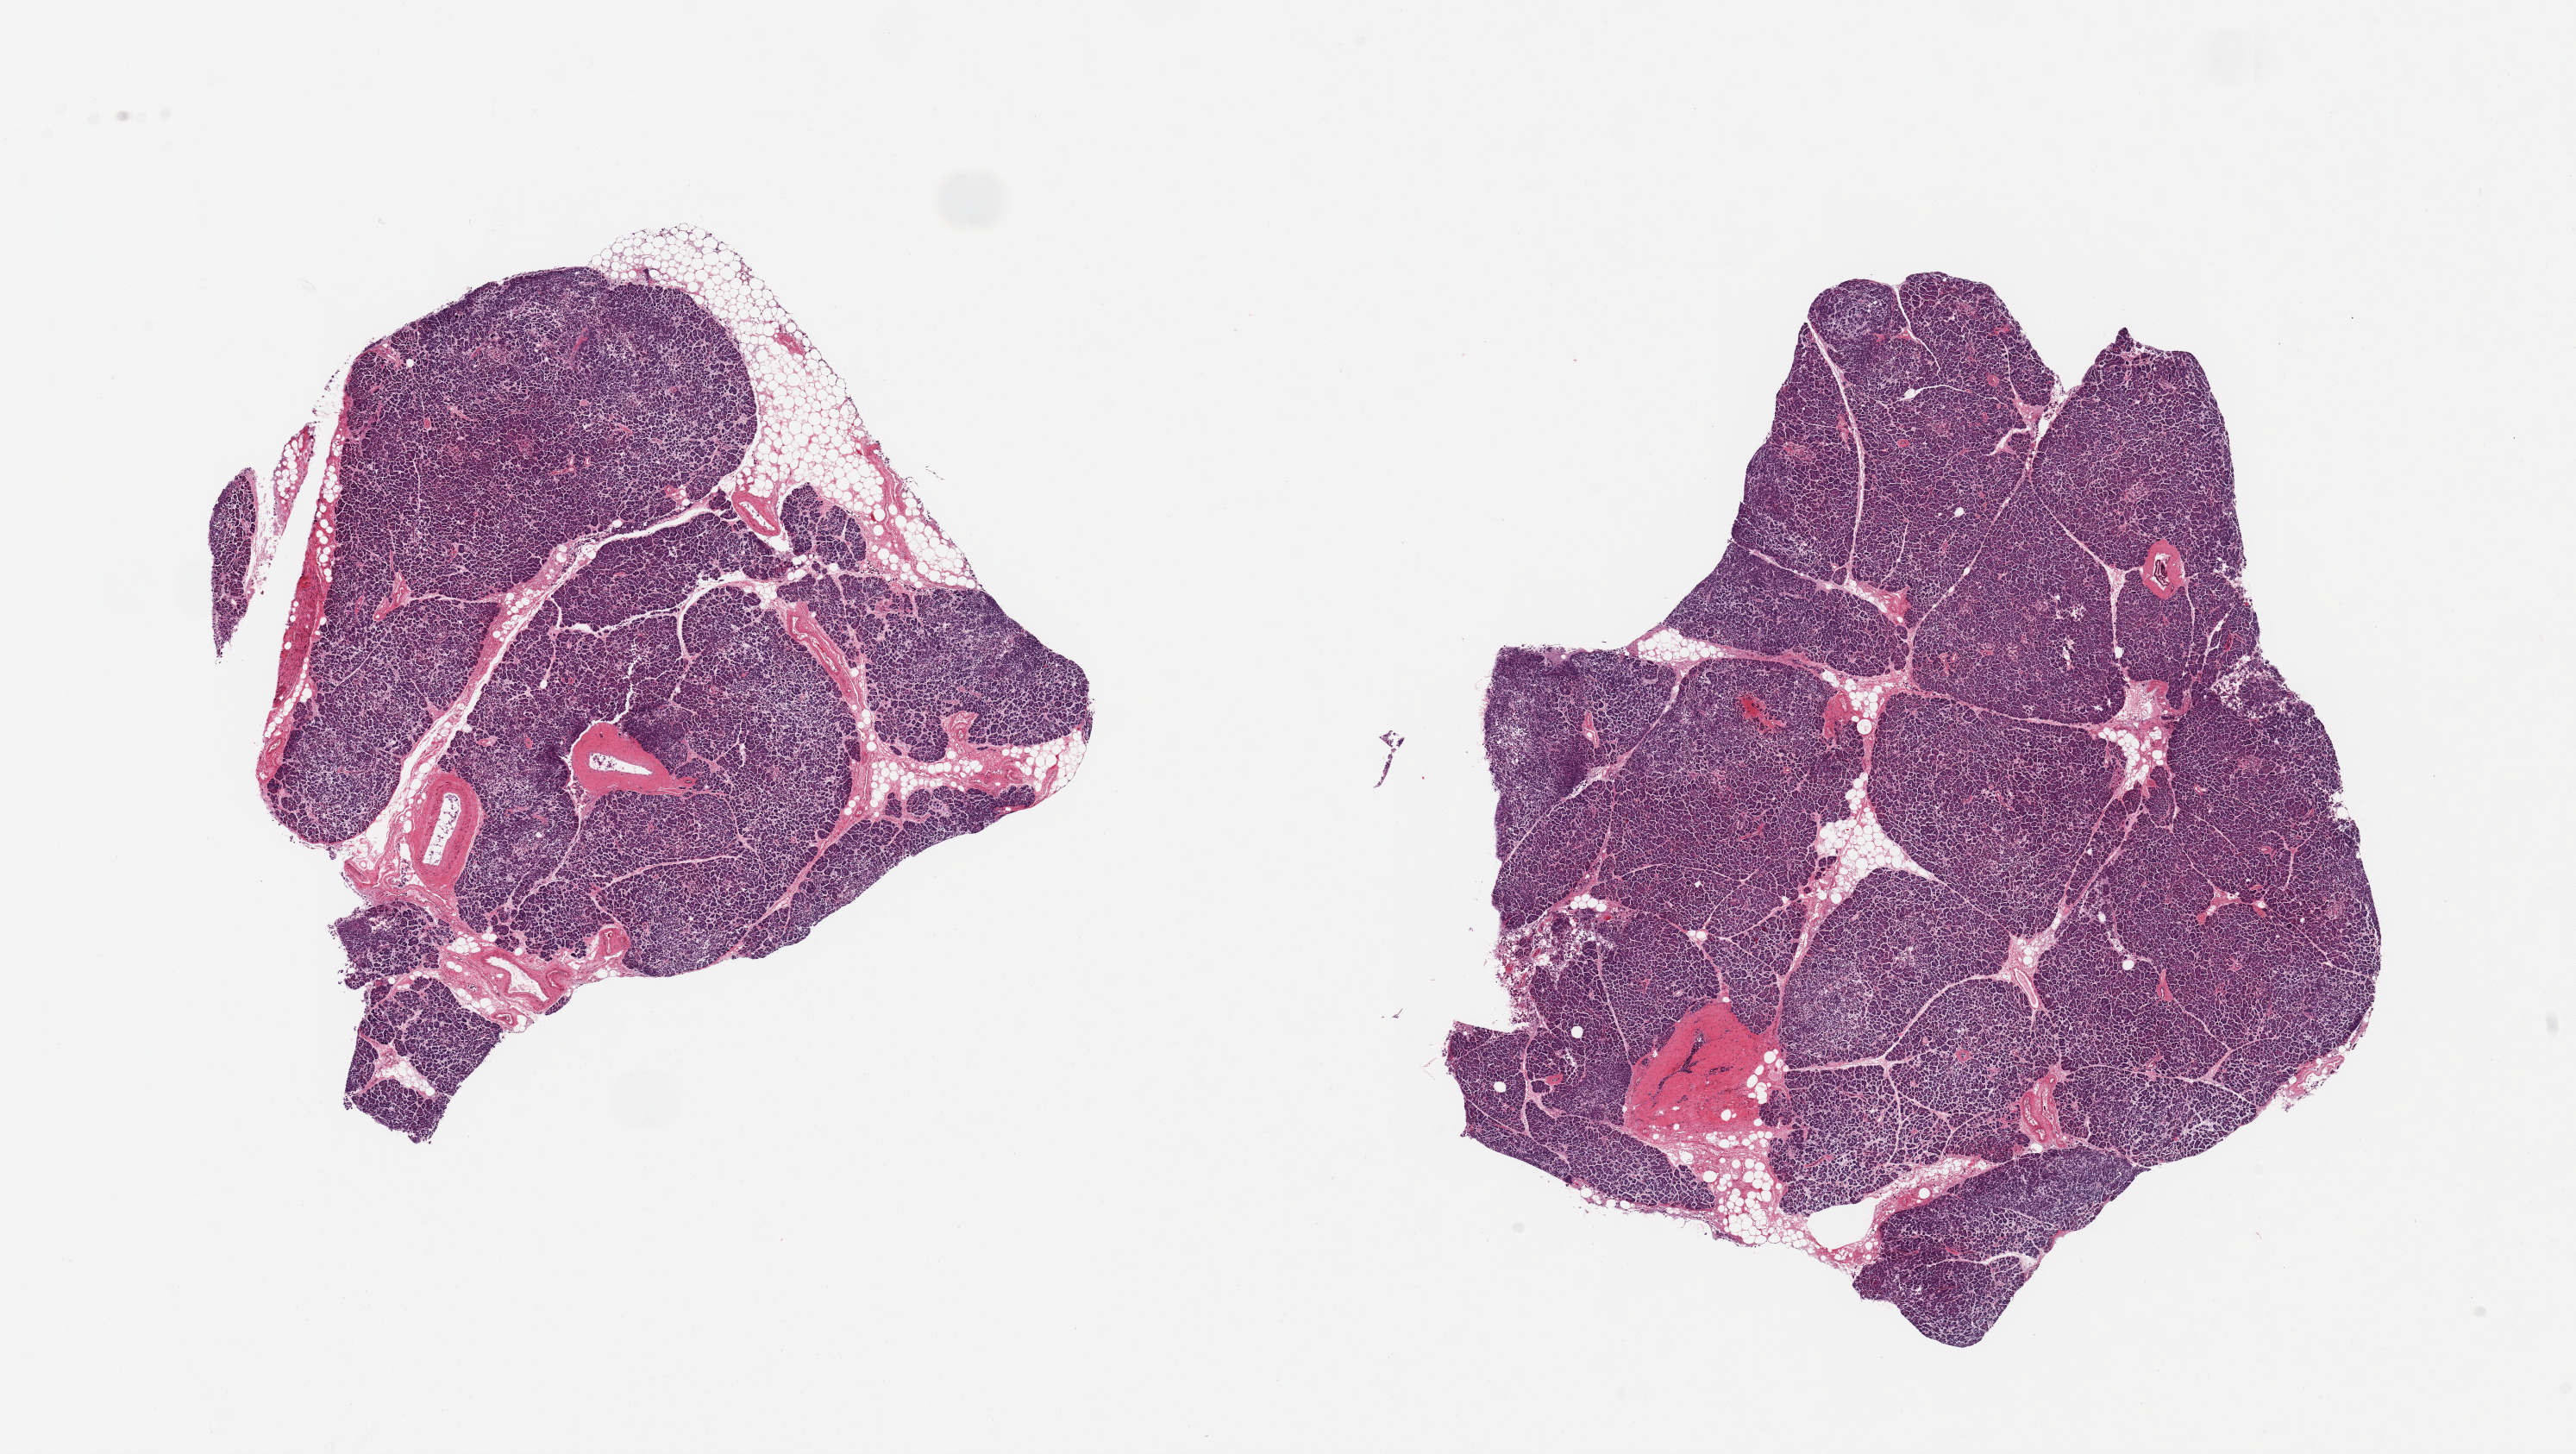
Digitized H&E-stained section, brightfield, shown as a low-resolution overview of the whole scanned area (about 23.6 x 13.3 mm, slide scanned at 20x); PAXgene-fixed paraffin-embedded (PFPE) section; section of pancreas (target tissue); donor tissue sample. Donor sex: male.
Review note (as recorded): 2 pieces, moderate saponification; Islets not well visualized.